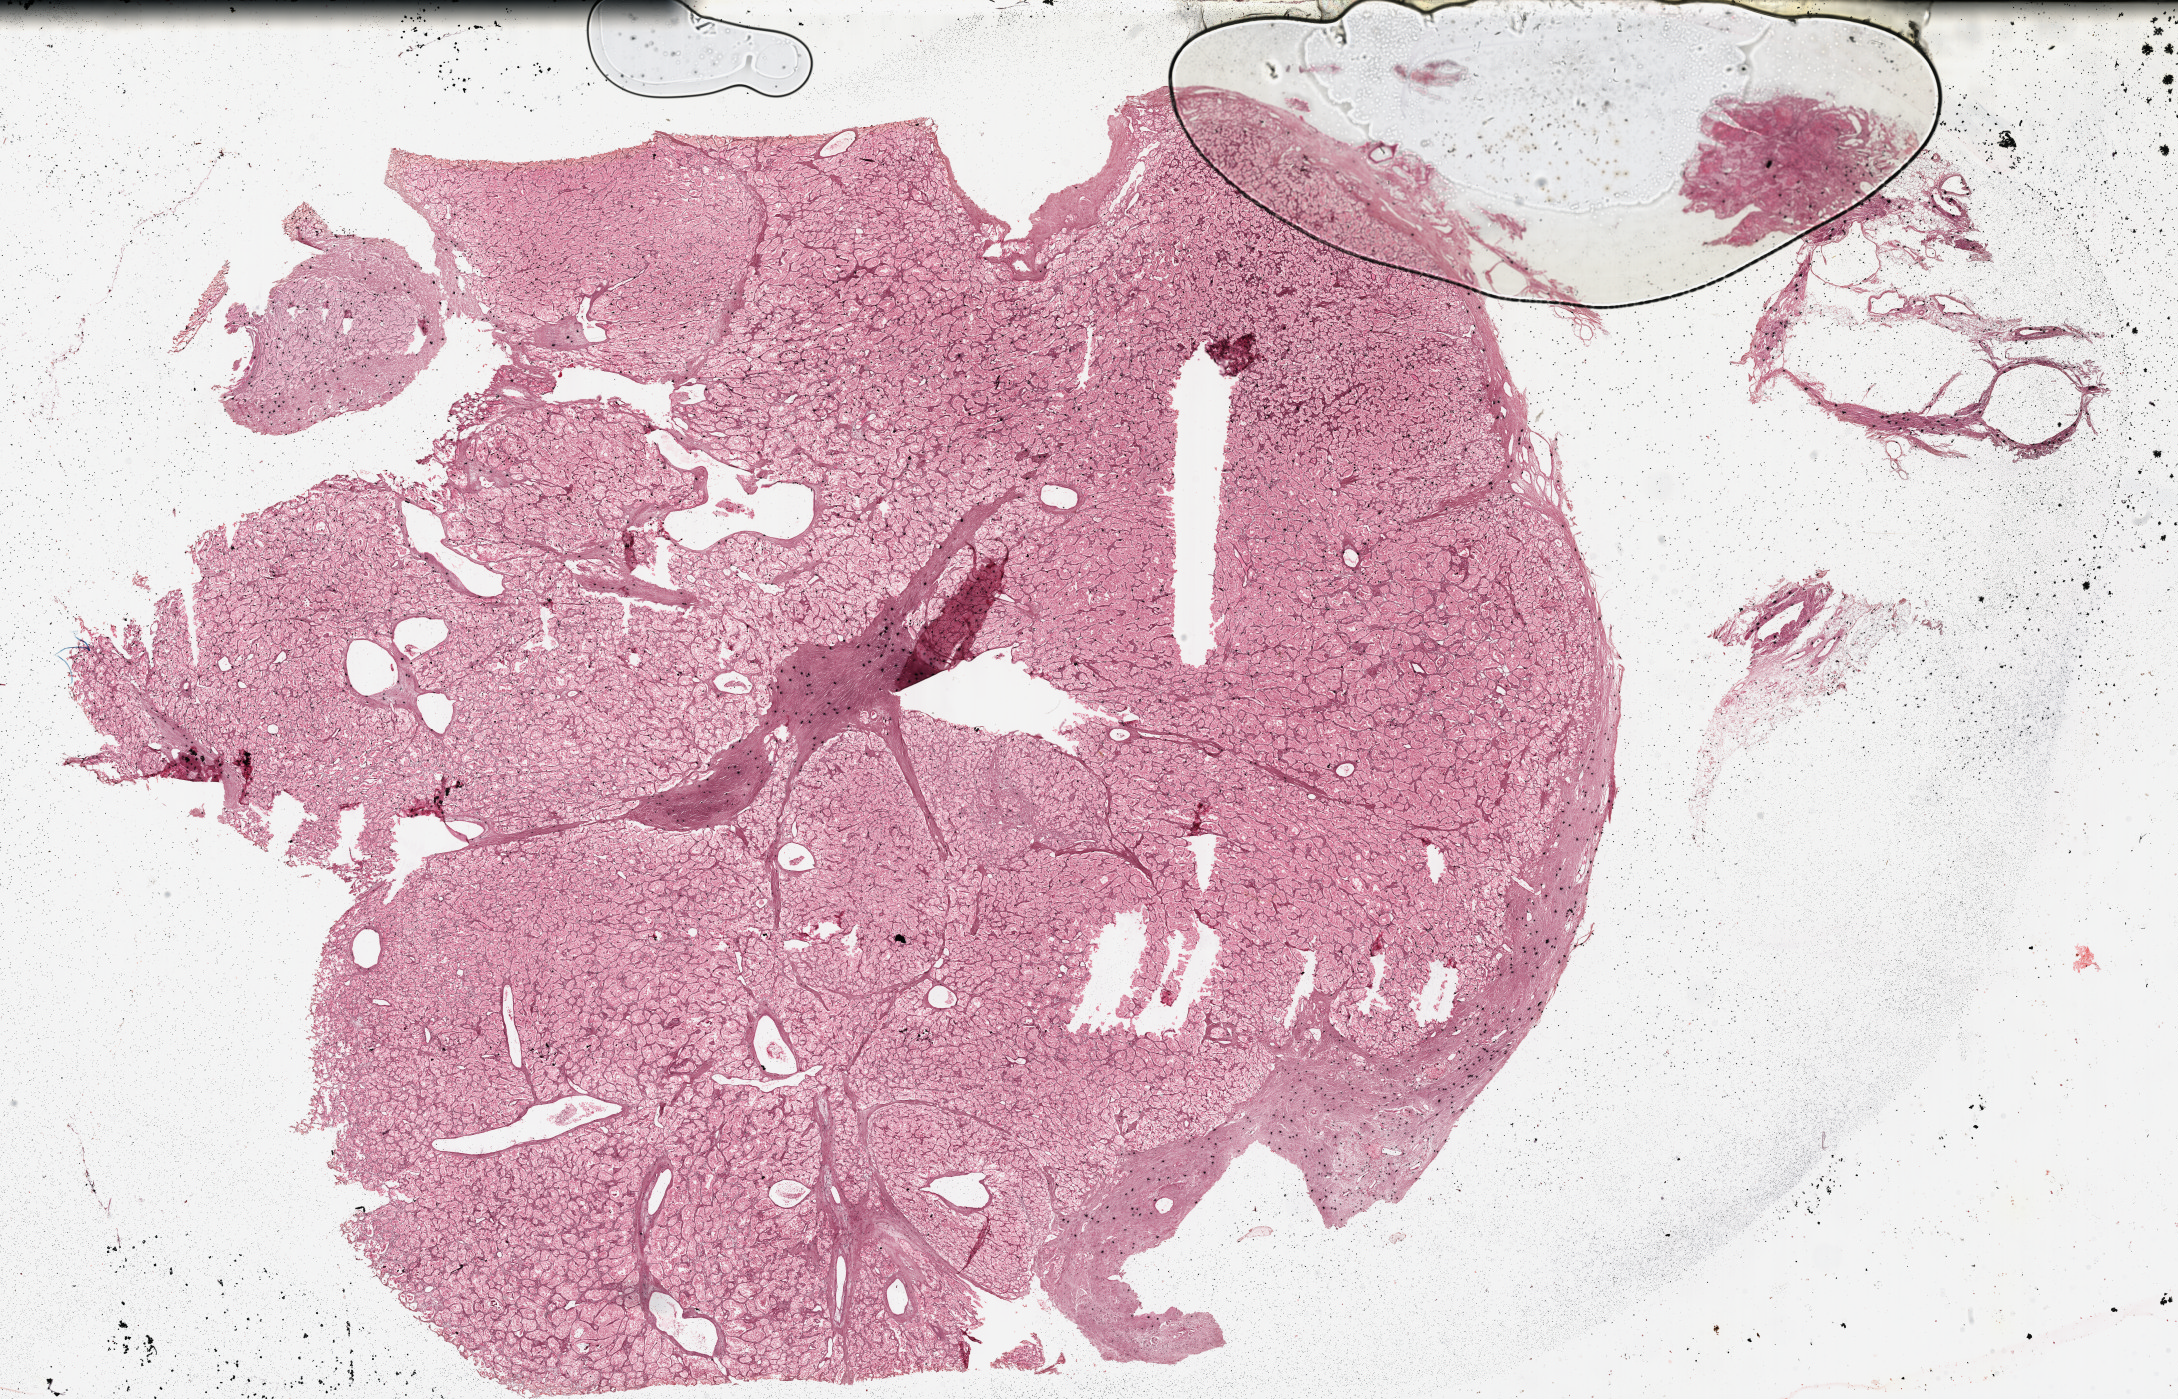
Digitized Hematoxylin and eosin (H&E) stained tissue section (whole slide) — whole scanned area (about 35.2 x 22.6 mm) shown as a low-resolution overview; FFPE section; retroperitoneum and peritoneum, primary tumour sample. Male, age 20 years at initial diagnosis.
• histologic diagnosis: Extra-adrenal paraganglioma, malignant